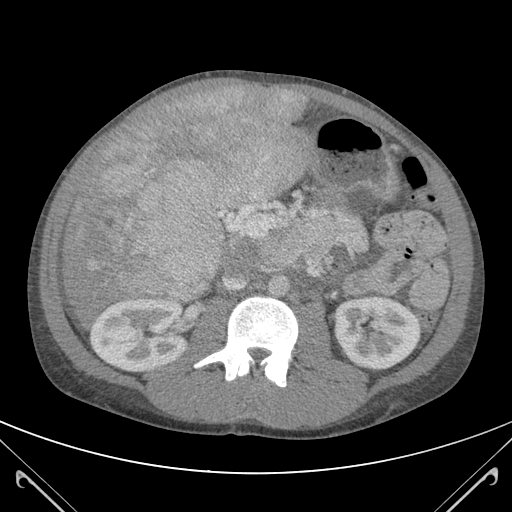
Contrast-enhanced abdominal CT (liver protocol), one axial slice; slice 53 of 118 in the series (ordered by position); 120 kVp; soft-tissue window (W 400 / L 40 HU); 3 mm slice thickness; 512 × 512 image matrix. Case-level facts recorded for this patient, not image findings: diagnosis: hepatocellular carcinoma (patient treated with transarterial chemoembolisation; whether this scan precedes or follows treatment is not stated here); TNM stage (as recorded): Stage-IIIB; Child-Pugh class: A; tumour nodularity: uninodular.
Annotated regions visible in this slice (semi-automatic segmentation, software-assisted and operator-edited):
- abdominal aorta: bounding box [x1, y1, x2, y2] px = [269, 277, 288, 296]
- liver parenchyma outside the tumour (the mass and vessels are separate outlines, so this box may not span the whole liver): [58, 84, 317, 323]
- mass: [79, 87, 312, 303]
- liver vessels: [148, 104, 277, 302]